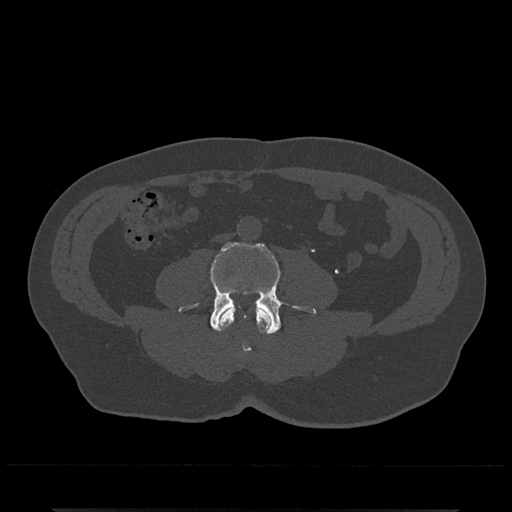
CT including the spine, one axial slice. Position 174 of 797 along the scan axis. Reconstruction kernel Br40s/3. 120 kVp. Bone window (W 1800 / L 400 HU). 0.5 mm slice thickness. 512 × 512 image matrix. Patient: male, 67 years. From the clinical record (not read from this slice): primary cancer: prostate.
Structures marked on this image (semi-automatically segmented with operator editing):
- L3 vertebra: bounding box (x1, y1, x2, y2) in pixels: (218, 307, 272, 354)
- L4 vertebra: (179, 242, 317, 334)